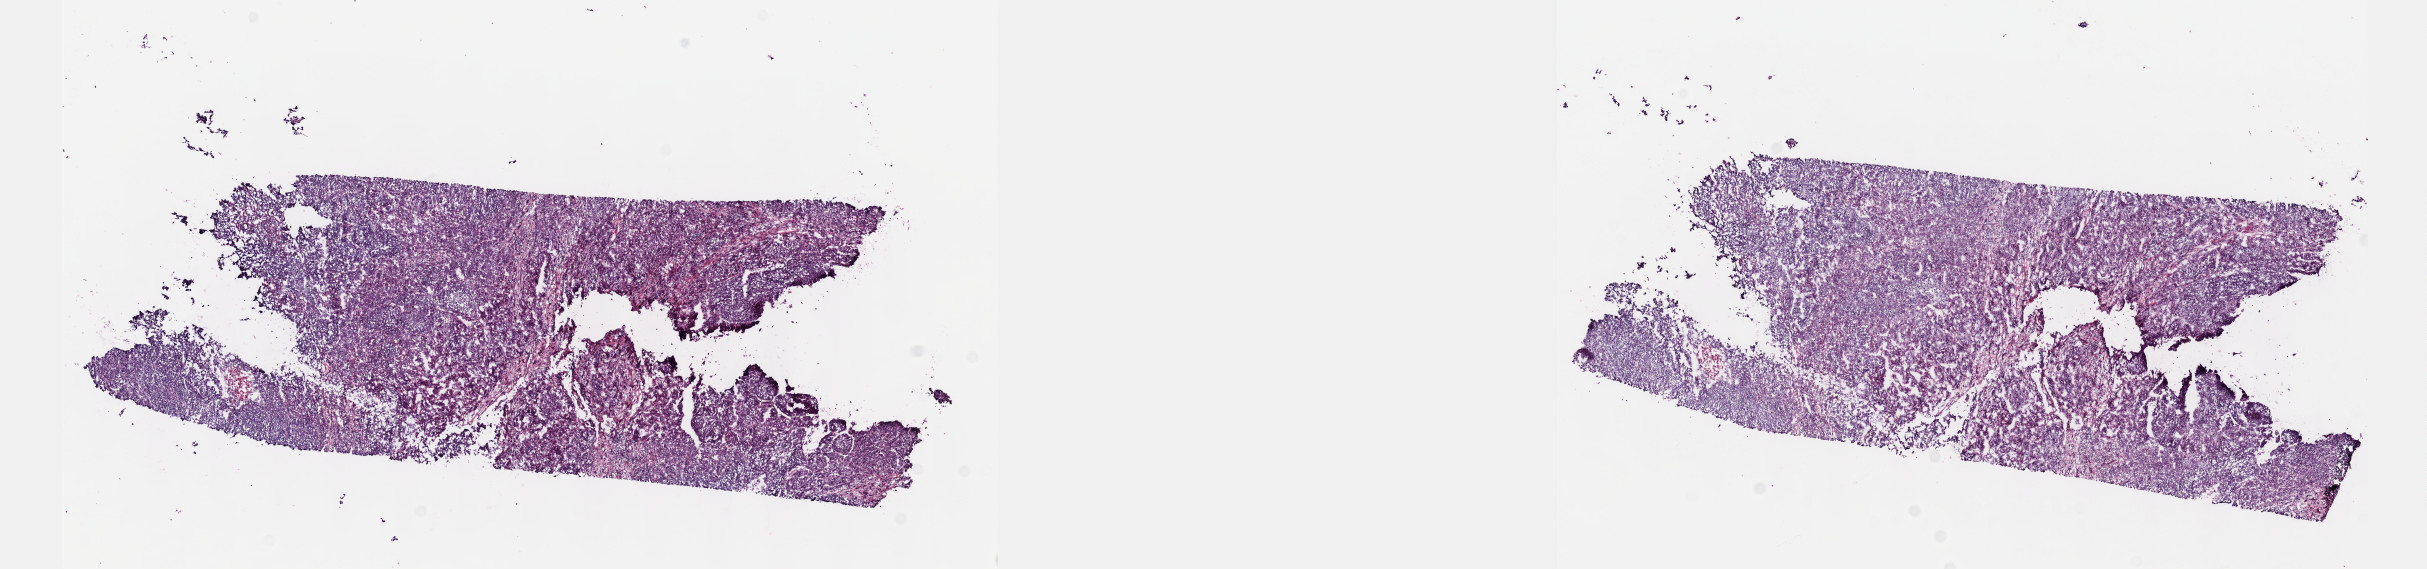
Whole-slide histology image, Hematoxylin and eosin (H&E) stained, a low-resolution overview of the entire scanned area, about 19.6 x 4.6 mm, frozen section from the top of the tissue portion, primary tumour sample from the liver. Male patient; age at initial diagnosis 57 years. Histologic grade: G2 (moderately differentiated). Slide review estimates, as recorded: tumour cells 100%, tumour nuclei 80%, normal cells 0%, stromal cells 0%, necrosis 0%. Infiltration values recorded for this section: lymphocyte infiltration 2%, monocyte infiltration 0%, neutrophil infiltration 0%.
Pathologic diagnosis: Hepatocellular carcinoma, NOS. AJCC pathologic stage: IIIA.